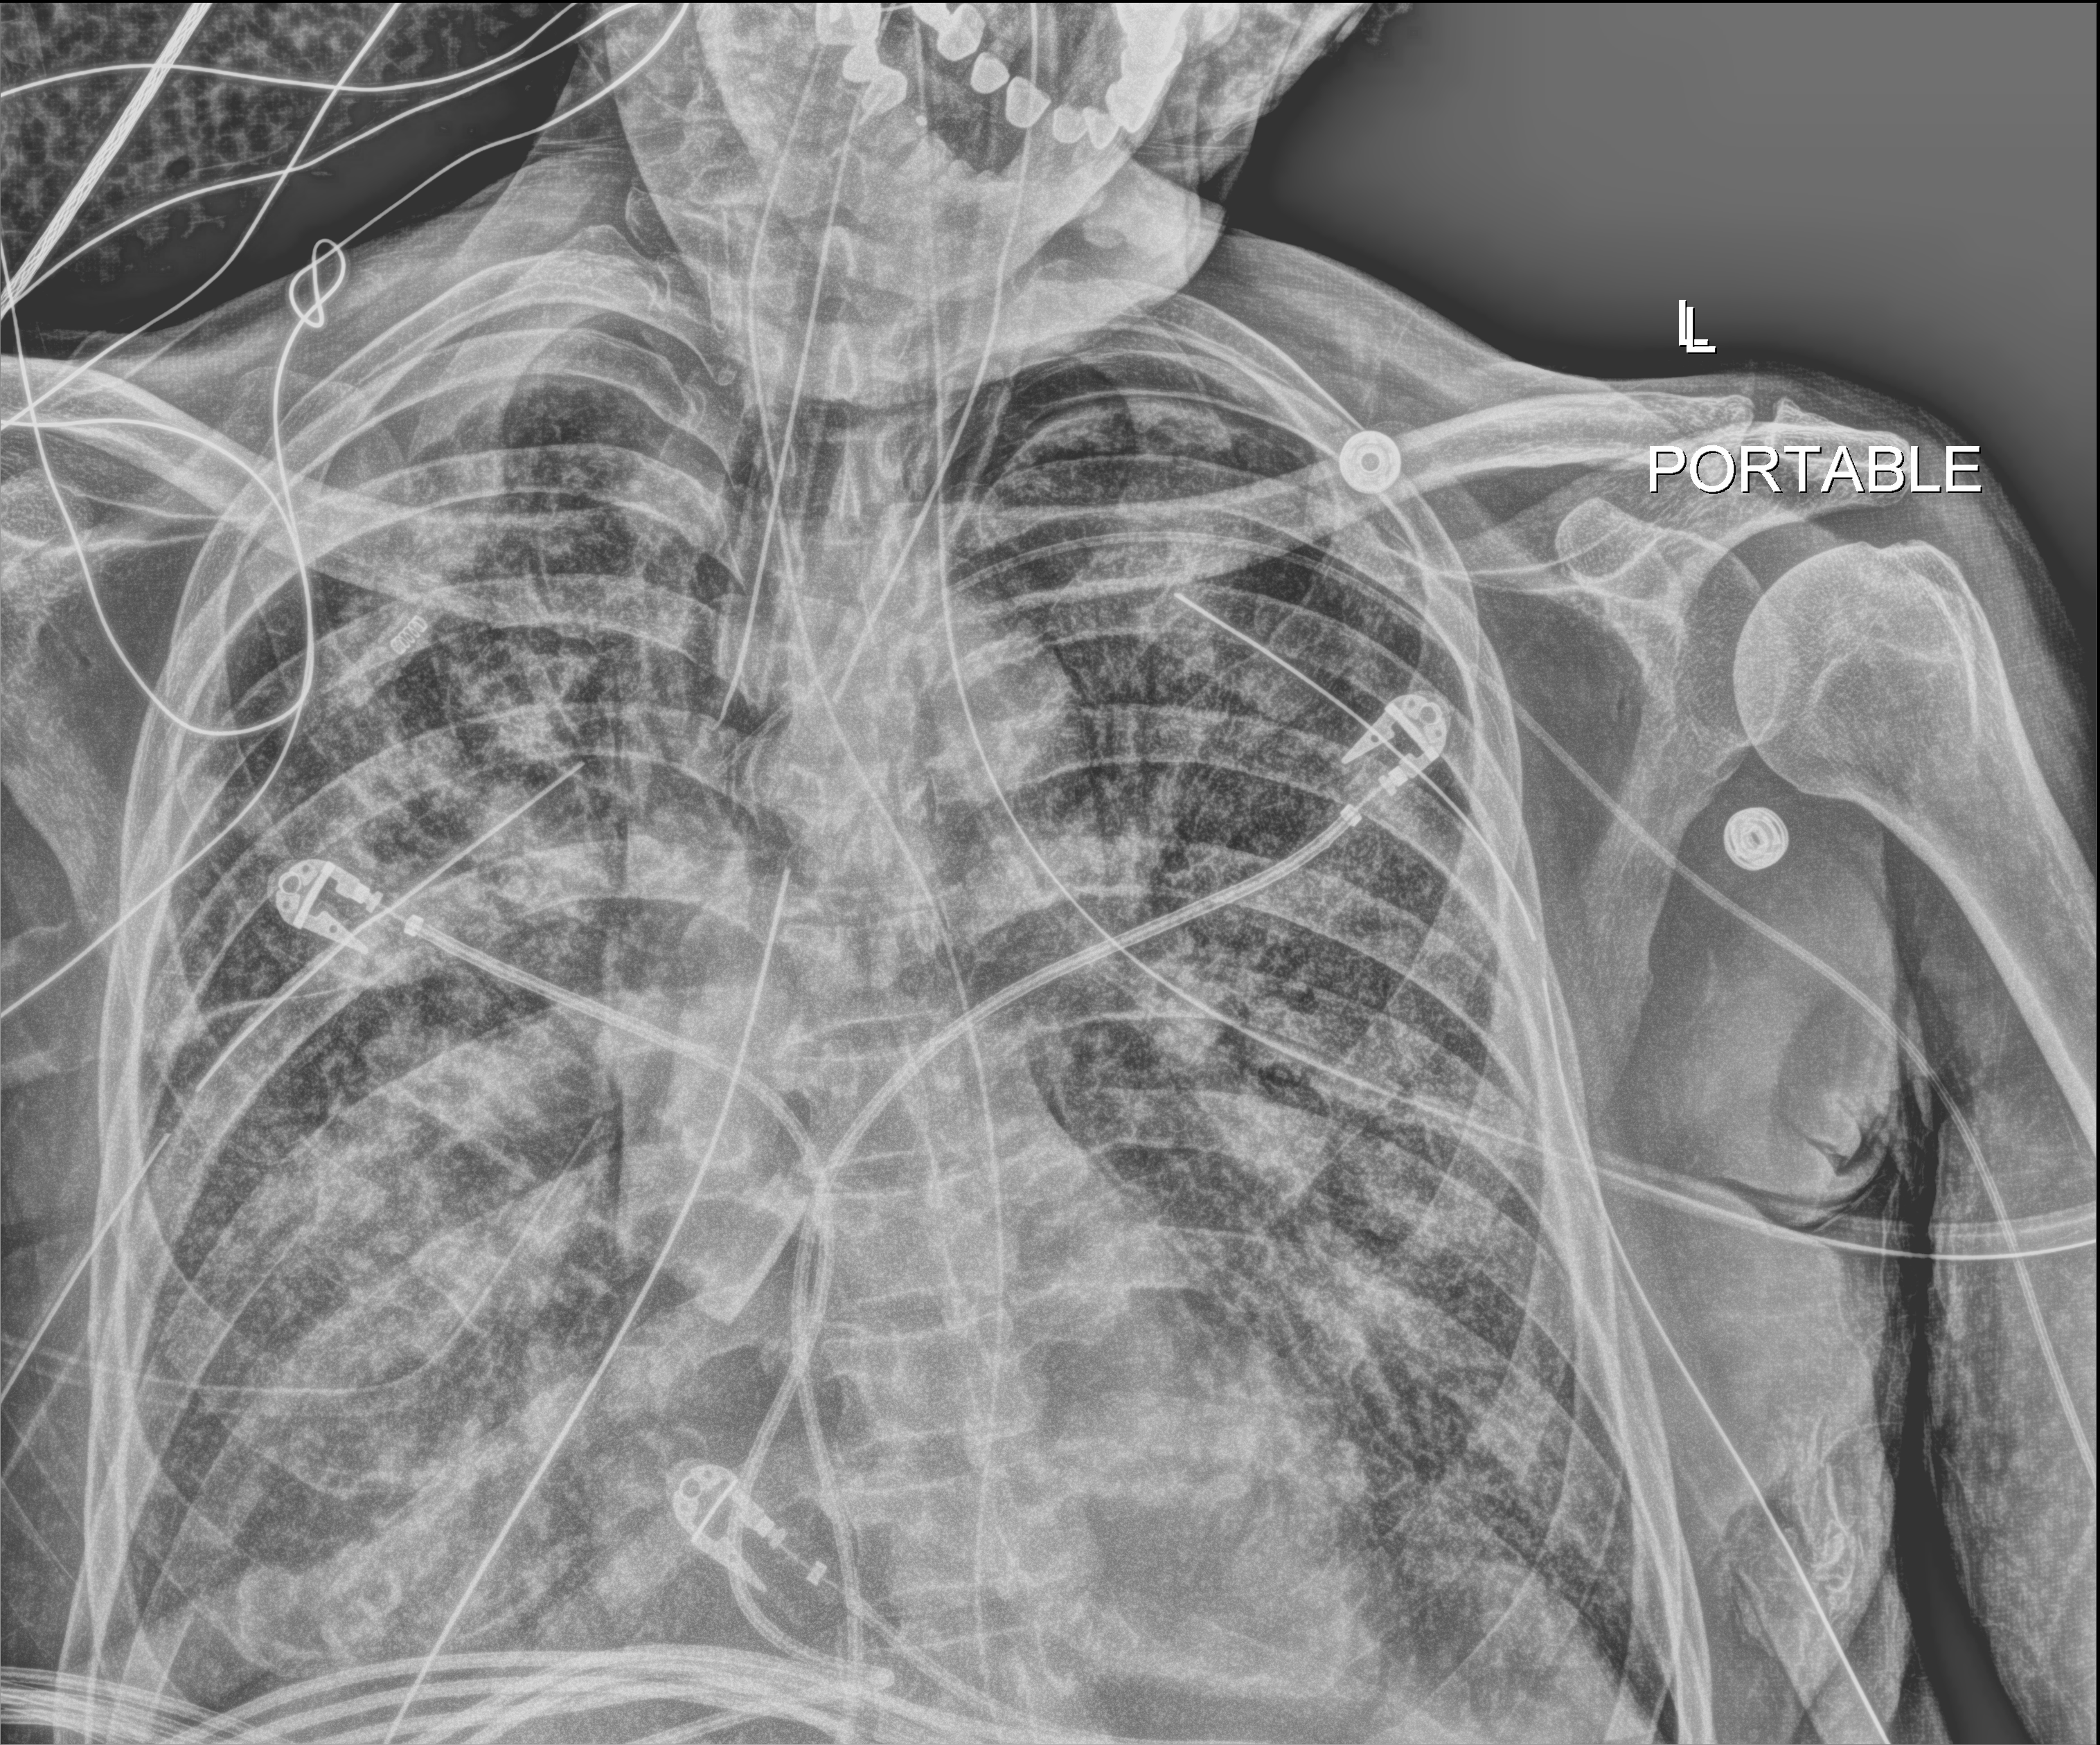
Bedside chest radiograph (digital radiography); anteroposterior (AP) projection. Patient hospitalised with COVID-19; male, aged 60–74 years.
Hospital-stay facts (about this admission, not read from this image; timing relative to this image not recorded):
- mechanically ventilated during this hospital stay: yes
- length of hospital stay: 31 days
- admitted to intensive care during this hospital stay: yes